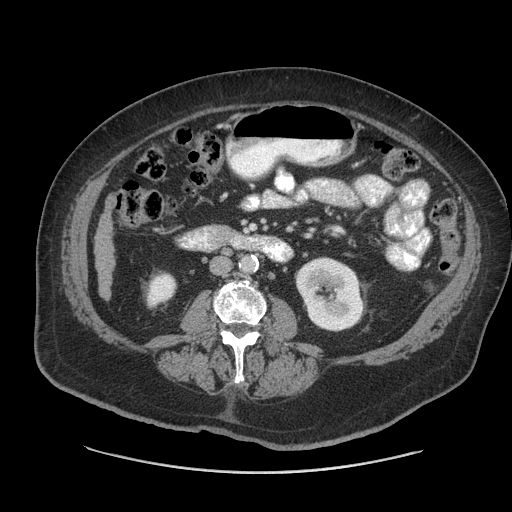
Contrast-enhanced abdominal CT (liver protocol), one axial slice. Slice 11 of 91 in the series (ordered by position). Reconstruction kernel STANDARD. 140 kVp. Soft-tissue window (W 400 / L 40 HU). 2.5 mm slice thickness. 512 × 512 image matrix, field of view 420 × 420 mm. From the clinical record (not read from this slice): diagnosis: hepatocellular carcinoma (patient treated with transarterial chemoembolisation; whether this scan precedes or follows treatment is not stated here); TNM stage (as recorded): Stage-I.
Annotated regions visible in this slice (semi-automatically segmented with operator editing):
- liver parenchyma outside the tumour (the mass and vessels are separate outlines, so this box may not span the whole liver): bounding box [x1, y1, x2, y2] px = [94, 211, 114, 298]